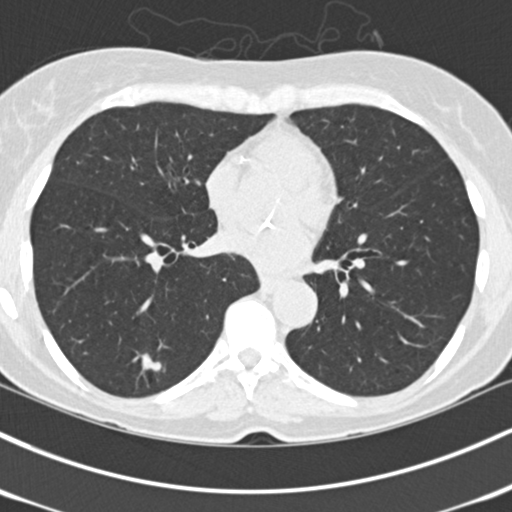
Low-dose screening chest CT, one axial slice. Slice 63 of 150 in the series (ordered by position). Reconstruction kernel B30f. 120 kVp. Lung window (W 1500 / L -600 HU). 2 mm slice thickness. 512 × 512 image matrix, field of view 318 × 318 mm.
Structures marked on this image (outlined manually by an expert reader):
- lesion 1 (tumor): bounding box (x1, y1, x2, y2) in pixels: (142, 354, 161, 371)